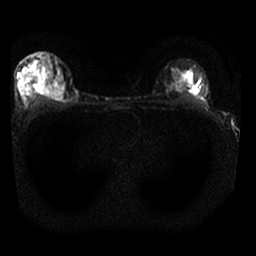
Breast MRI, one axial slice. Position 20 of 25 along the scan axis. Diffusion-weighted series; image 2 of 4 stored at this slice position (different b-values; order by instance number). 1.5 T. 4 mm slice thickness. 256 × 256 image matrix, field of view 310 × 310 mm. Female patient.
Annotated regions visible in this slice (outlined manually by an expert reader):
- tumour on diffusion-weighted imaging: bounding box [x1, y1, x2, y2] px = [38, 78, 63, 98]